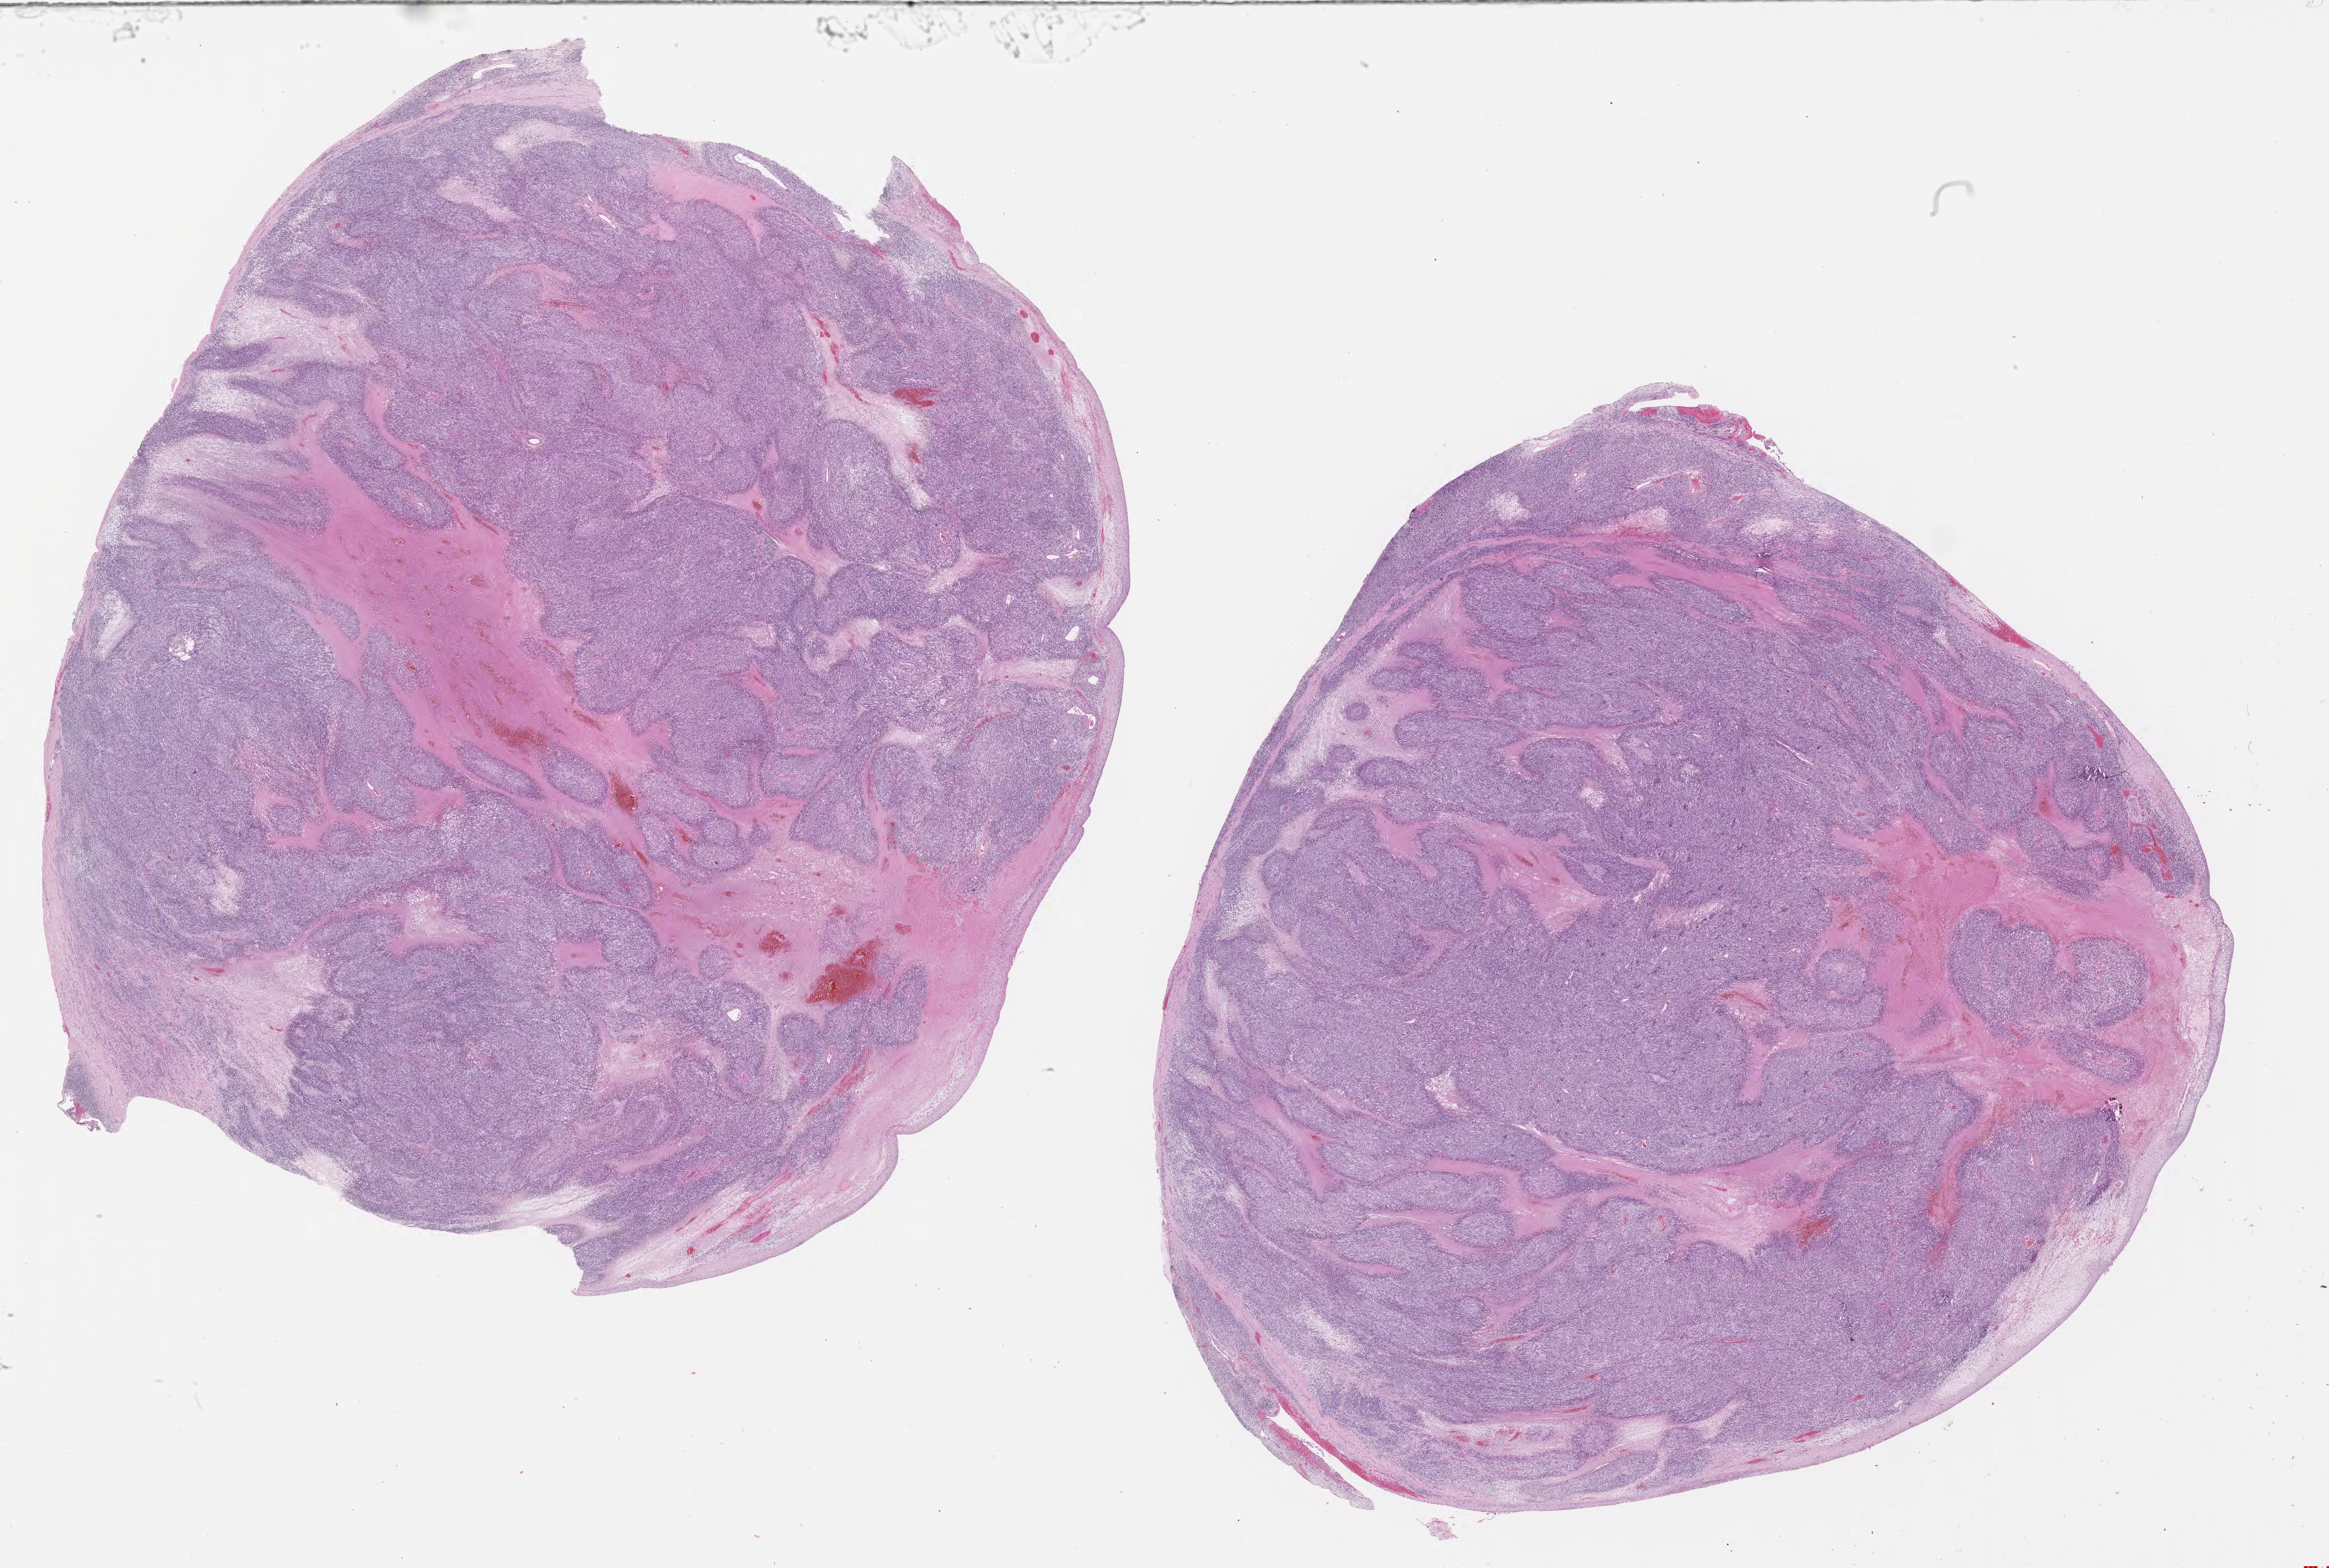
Digitized H&E-stained section of tumor tissue, whole scanned area (about 31.2 x 21.0 mm) shown as a low-resolution overview; FFPE section; site: soft tissue - testicle, right. Male patient, age at diagnosis 8.2 years.
Stage (as recorded): 1. Metastatic status at presentation (as recorded): non-metastatic. Diagnosis: rhabdomyosarcoma; histological classification: embryonal rhabdomyosarcoma.